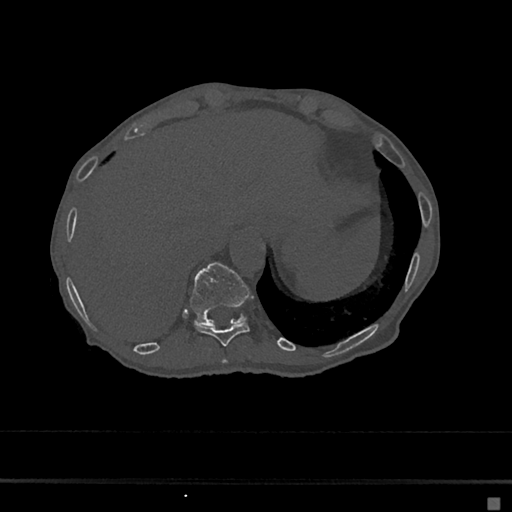
CT including the spine, one axial slice; 120 kVp; bone window (W 1800 / L 400 HU); 0.5 mm slice thickness; 512 × 512 image matrix, field of view 360 × 360 mm. Female patient, age 68 years. Case-level facts recorded for this patient, not image findings: primary cancer: renal.
Annotated regions visible in this slice (semi-automatically segmented with operator editing):
- T10 vertebra: bounding box [x1, y1, x2, y2] px = [194, 322, 249, 346]
- T11 vertebra: [190, 263, 250, 326]
- T9 vertebra: [221, 358, 227, 364]